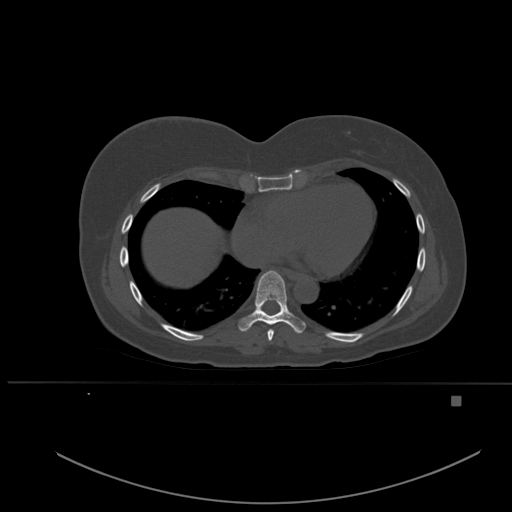
CT including the spine, one axial slice. Bone window (W 1800 / L 400 HU). 512 × 512 image matrix, field of view 443 × 443 mm. Female patient, age 49 years. Case-level facts recorded for this patient, not image findings: primary cancer: breast; vertebrae with lytic lesions (as recorded): L3, T12, L4.
Outlined on this slice (semi-automatic segmentation, software-assisted and operator-edited):
- T7 vertebra: bounding box [x1, y1, x2, y2] px = [267, 329, 274, 341]
- T8 vertebra: [238, 270, 306, 334]